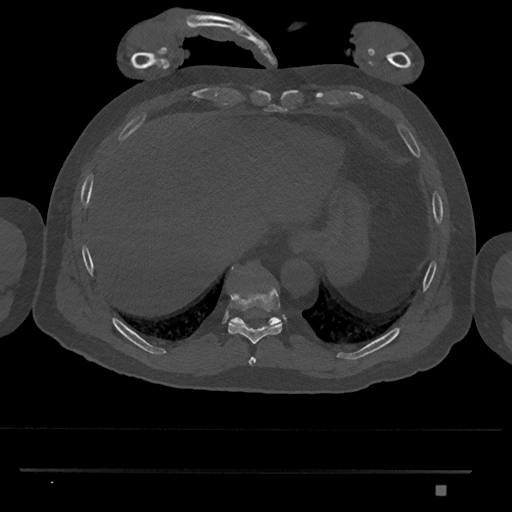
CT including the spine, one axial slice; slice 1042 of 1134 in the series (ordered by position); reconstruction kernel Br40s/3; 120 kVp; bone window (W 1800 / L 400 HU); 512 × 512 image matrix, field of view 429 × 429 mm. Patient: male, 65 years. Case-level facts recorded for this patient, not image findings: primary cancer: prostate.
Outlined on this slice (semi-automatic segmentation, software-assisted and operator-edited):
- T10 vertebra: bounding box <231,269,282,326> (left, top, right, bottom; pixels)
- T8 vertebra: <248,357,256,365>
- T9 vertebra: <228,287,282,344>